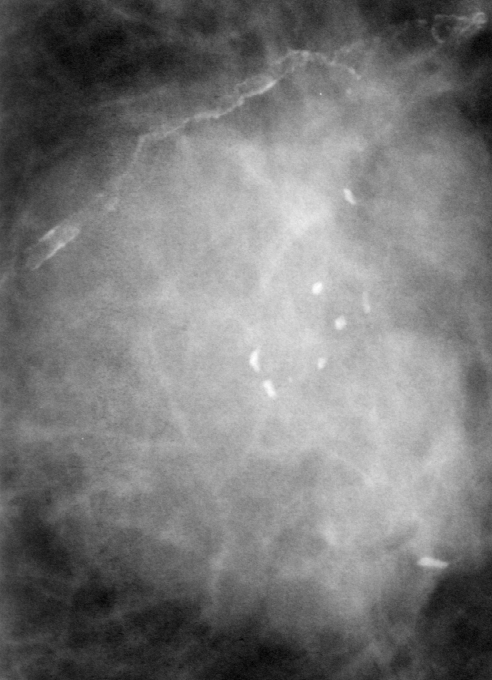
Cropped region of a digitized screen-film mammogram centred on a radiologist-marked abnormality; left breast; CC view.
- Finding: mass, shape lobulated, margins microlobulated; BI-RADS assessment category 5; subtlety rating 5 on a 1 (subtle) to 5 (obvious) scale; pathology (as recorded): malignant.